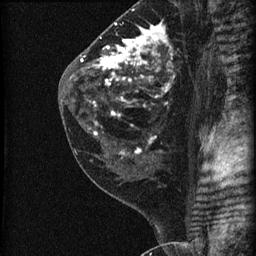
Breast MRI (dynamic contrast-enhanced), one sagittal slice; dynamic contrast-enhanced series, image 2 of 3 at this slice position (ordered by acquisition); 1.5 T; TE 4.2 ms, TR 22.7 ms; 1.8 mm slice thickness; 256 × 256 image matrix, field of view 180 × 180 mm. Female patient, age 45 years. From the clinical record (not read from this slice): setting: breast cancer imaged before/during neoadjuvant chemotherapy; receptor status: HR-positive, HER2-negative.
Structures marked on this image (semi-automatic segmentation, software-assisted and operator-edited):
- analysis volume of interest (the breast-tissue region the enhancement analysis was run in; not a lesion): bounding box (x1, y1, x2, y2) in pixels: (74, 11, 205, 140)
- tumour enhancement mask (voxels above the 90 % enhancement threshold inside the analysis volume of interest): (81, 23, 175, 140)